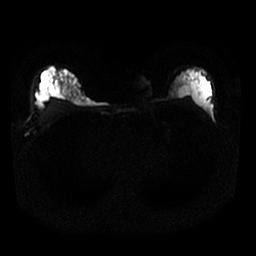
Breast MRI, one axial slice. Slice 20 of 25 in the series (ordered by position). Diffusion-weighted series; image 2 of 4 stored at this slice position (different b-values; order by instance number). 1.5 T. 256 × 256 image matrix. Female patient.
Structures marked on this image (expert manual segmentation):
- tumour on diffusion-weighted imaging: bounding box (x1, y1, x2, y2) in pixels: (173, 86, 179, 89)